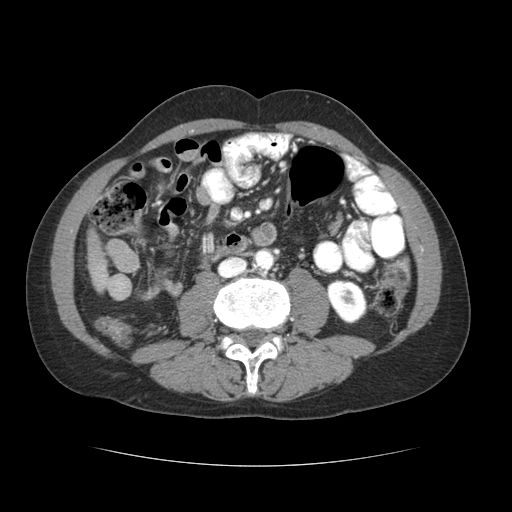
Contrast-enhanced abdominal CT (liver protocol), one axial slice; slice 5 of 69 in the series (ordered by position); reconstruction kernel STANDARD; soft-tissue window (W 400 / L 40 HU); 2.5 mm slice thickness; 512 × 512 image matrix, field of view 360 × 360 mm. Case-level facts recorded for this patient, not image findings: diagnosis: hepatocellular carcinoma (patient treated with transarterial chemoembolisation; whether this scan precedes or follows treatment is not stated here); TNM stage (as recorded): Stage-II; Child-Pugh class: B; tumour differentiation: poorly differentiated; tumour size: 2.6 cm.
Structures marked on this image (semi-automatic segmentation, software-assisted and operator-edited):
- liver parenchyma outside the tumour (the mass and vessels are separate outlines, so this box may not span the whole liver): bounding box [x1, y1, x2, y2] px = [88, 232, 130, 298]
- liver vessels: [103, 275, 124, 291]